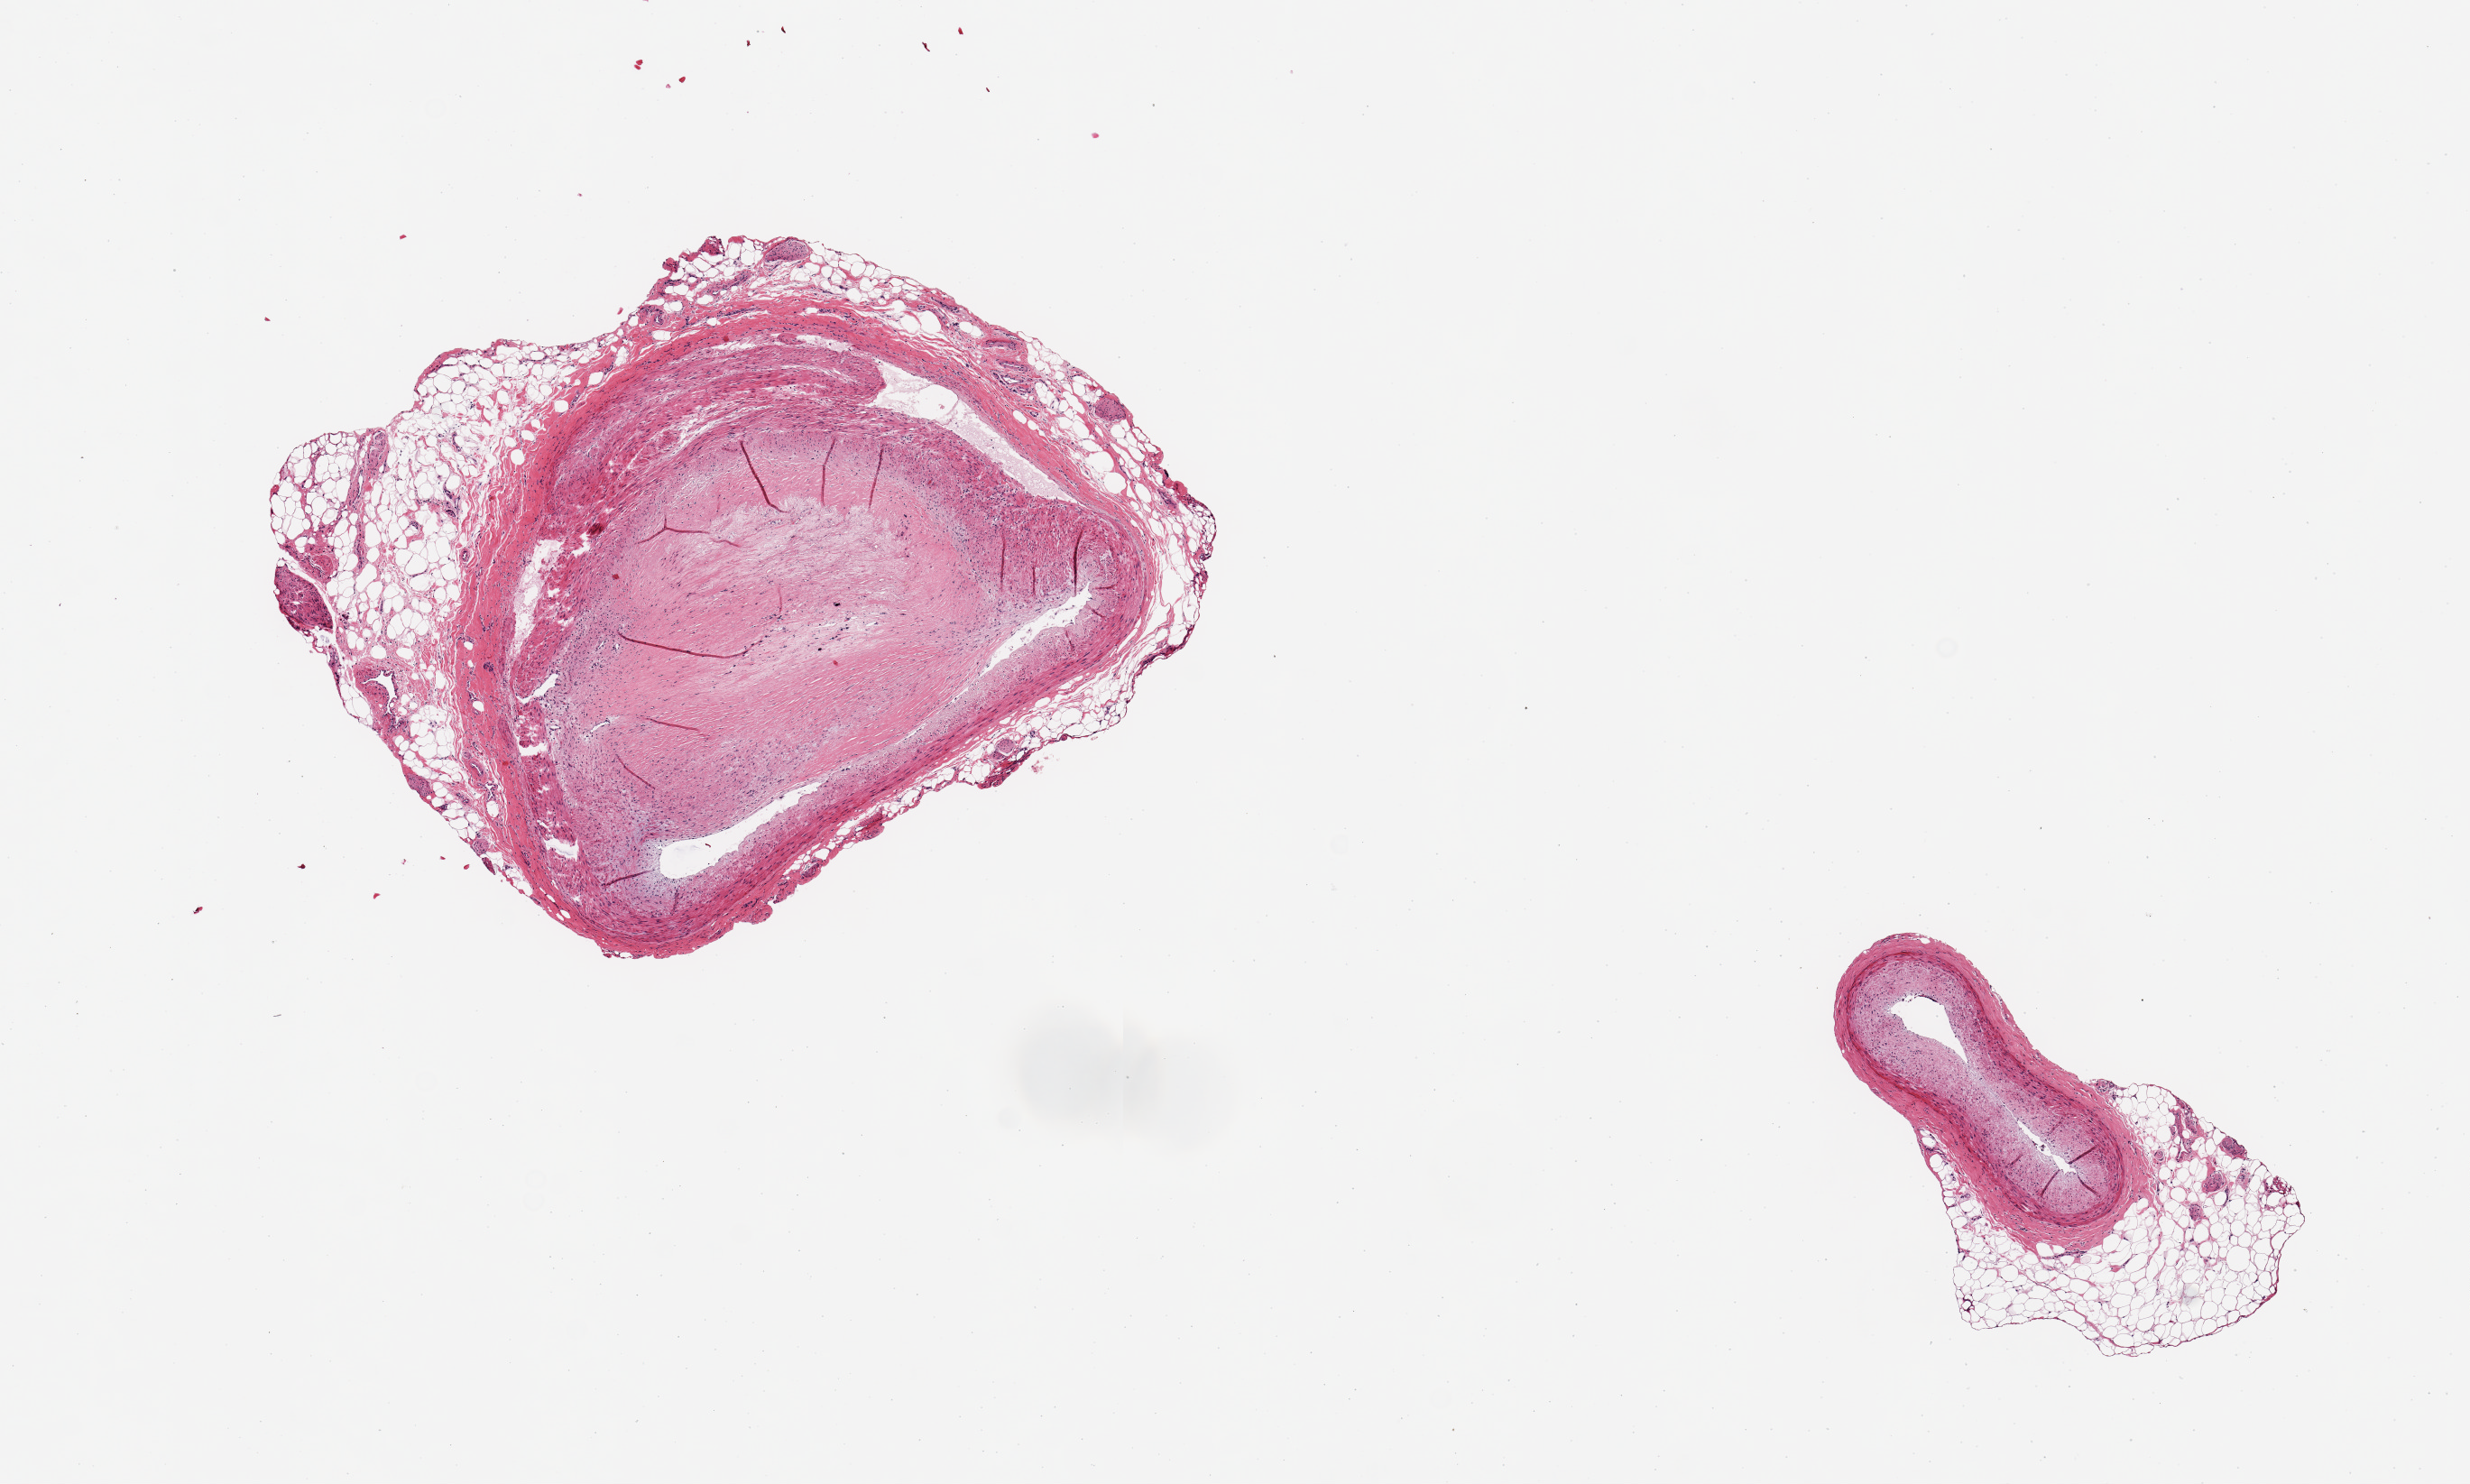
Hematoxylin and eosin (H&E) whole-slide image — low-resolution overview of the scanned area, about 10.8 x 6.5 mm (from a 20x scan); PAXgene-fixed paraffin-embedded (PFPE) section; sampled site (target tissue): coronary artery; donor tissue sample.
Review note (as recorded): 2 aliquots, one ~3x2mm, one 1.6x0.6mm. Larger aliquot with sub-total atherosclerotic occlusion.